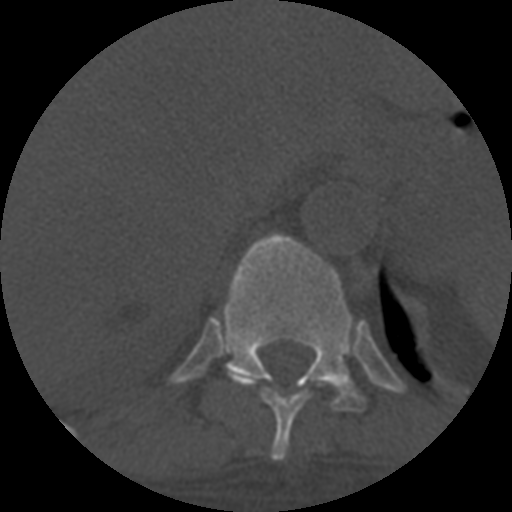
CT including the spine, one axial slice; slice 345 of 708 in the series (ordered by position); reconstruction kernel STANDARD; one of 3 acquisitions stored at this slice position; bone window (W 1800 / L 400 HU); 512 × 512 image matrix, field of view 160 × 160 mm. Patient age 55 years. From the clinical record (not read from this slice): primary cancer: colon; vertebrae with lytic lesions (as recorded): T12, L1, L5.
Annotated regions visible in this slice (semi-automatic segmentation, software-assisted and operator-edited):
- T10 vertebra: bounding box <227,371,311,461> (left, top, right, bottom; pixels)
- T11 vertebra: <223,232,368,413>